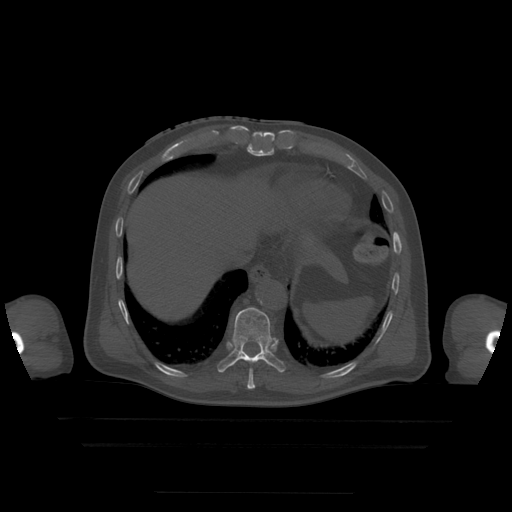
CT including the spine, one axial slice; slice 245 of 522 in the series (ordered by position); bone window (W 1800 / L 400 HU); 1.25 mm slice thickness; 512 × 512 image matrix, field of view 436 × 436 mm. Patient age 68 years. From the clinical record (not read from this slice): primary cancer: urothelial.
Structures marked on this image (semi-automatic segmentation, software-assisted and operator-edited):
- T10 vertebra: box from (x=218, y=307) to (x=286, y=373) px
- T9 vertebra: (x=247, y=369)–(x=255, y=390)